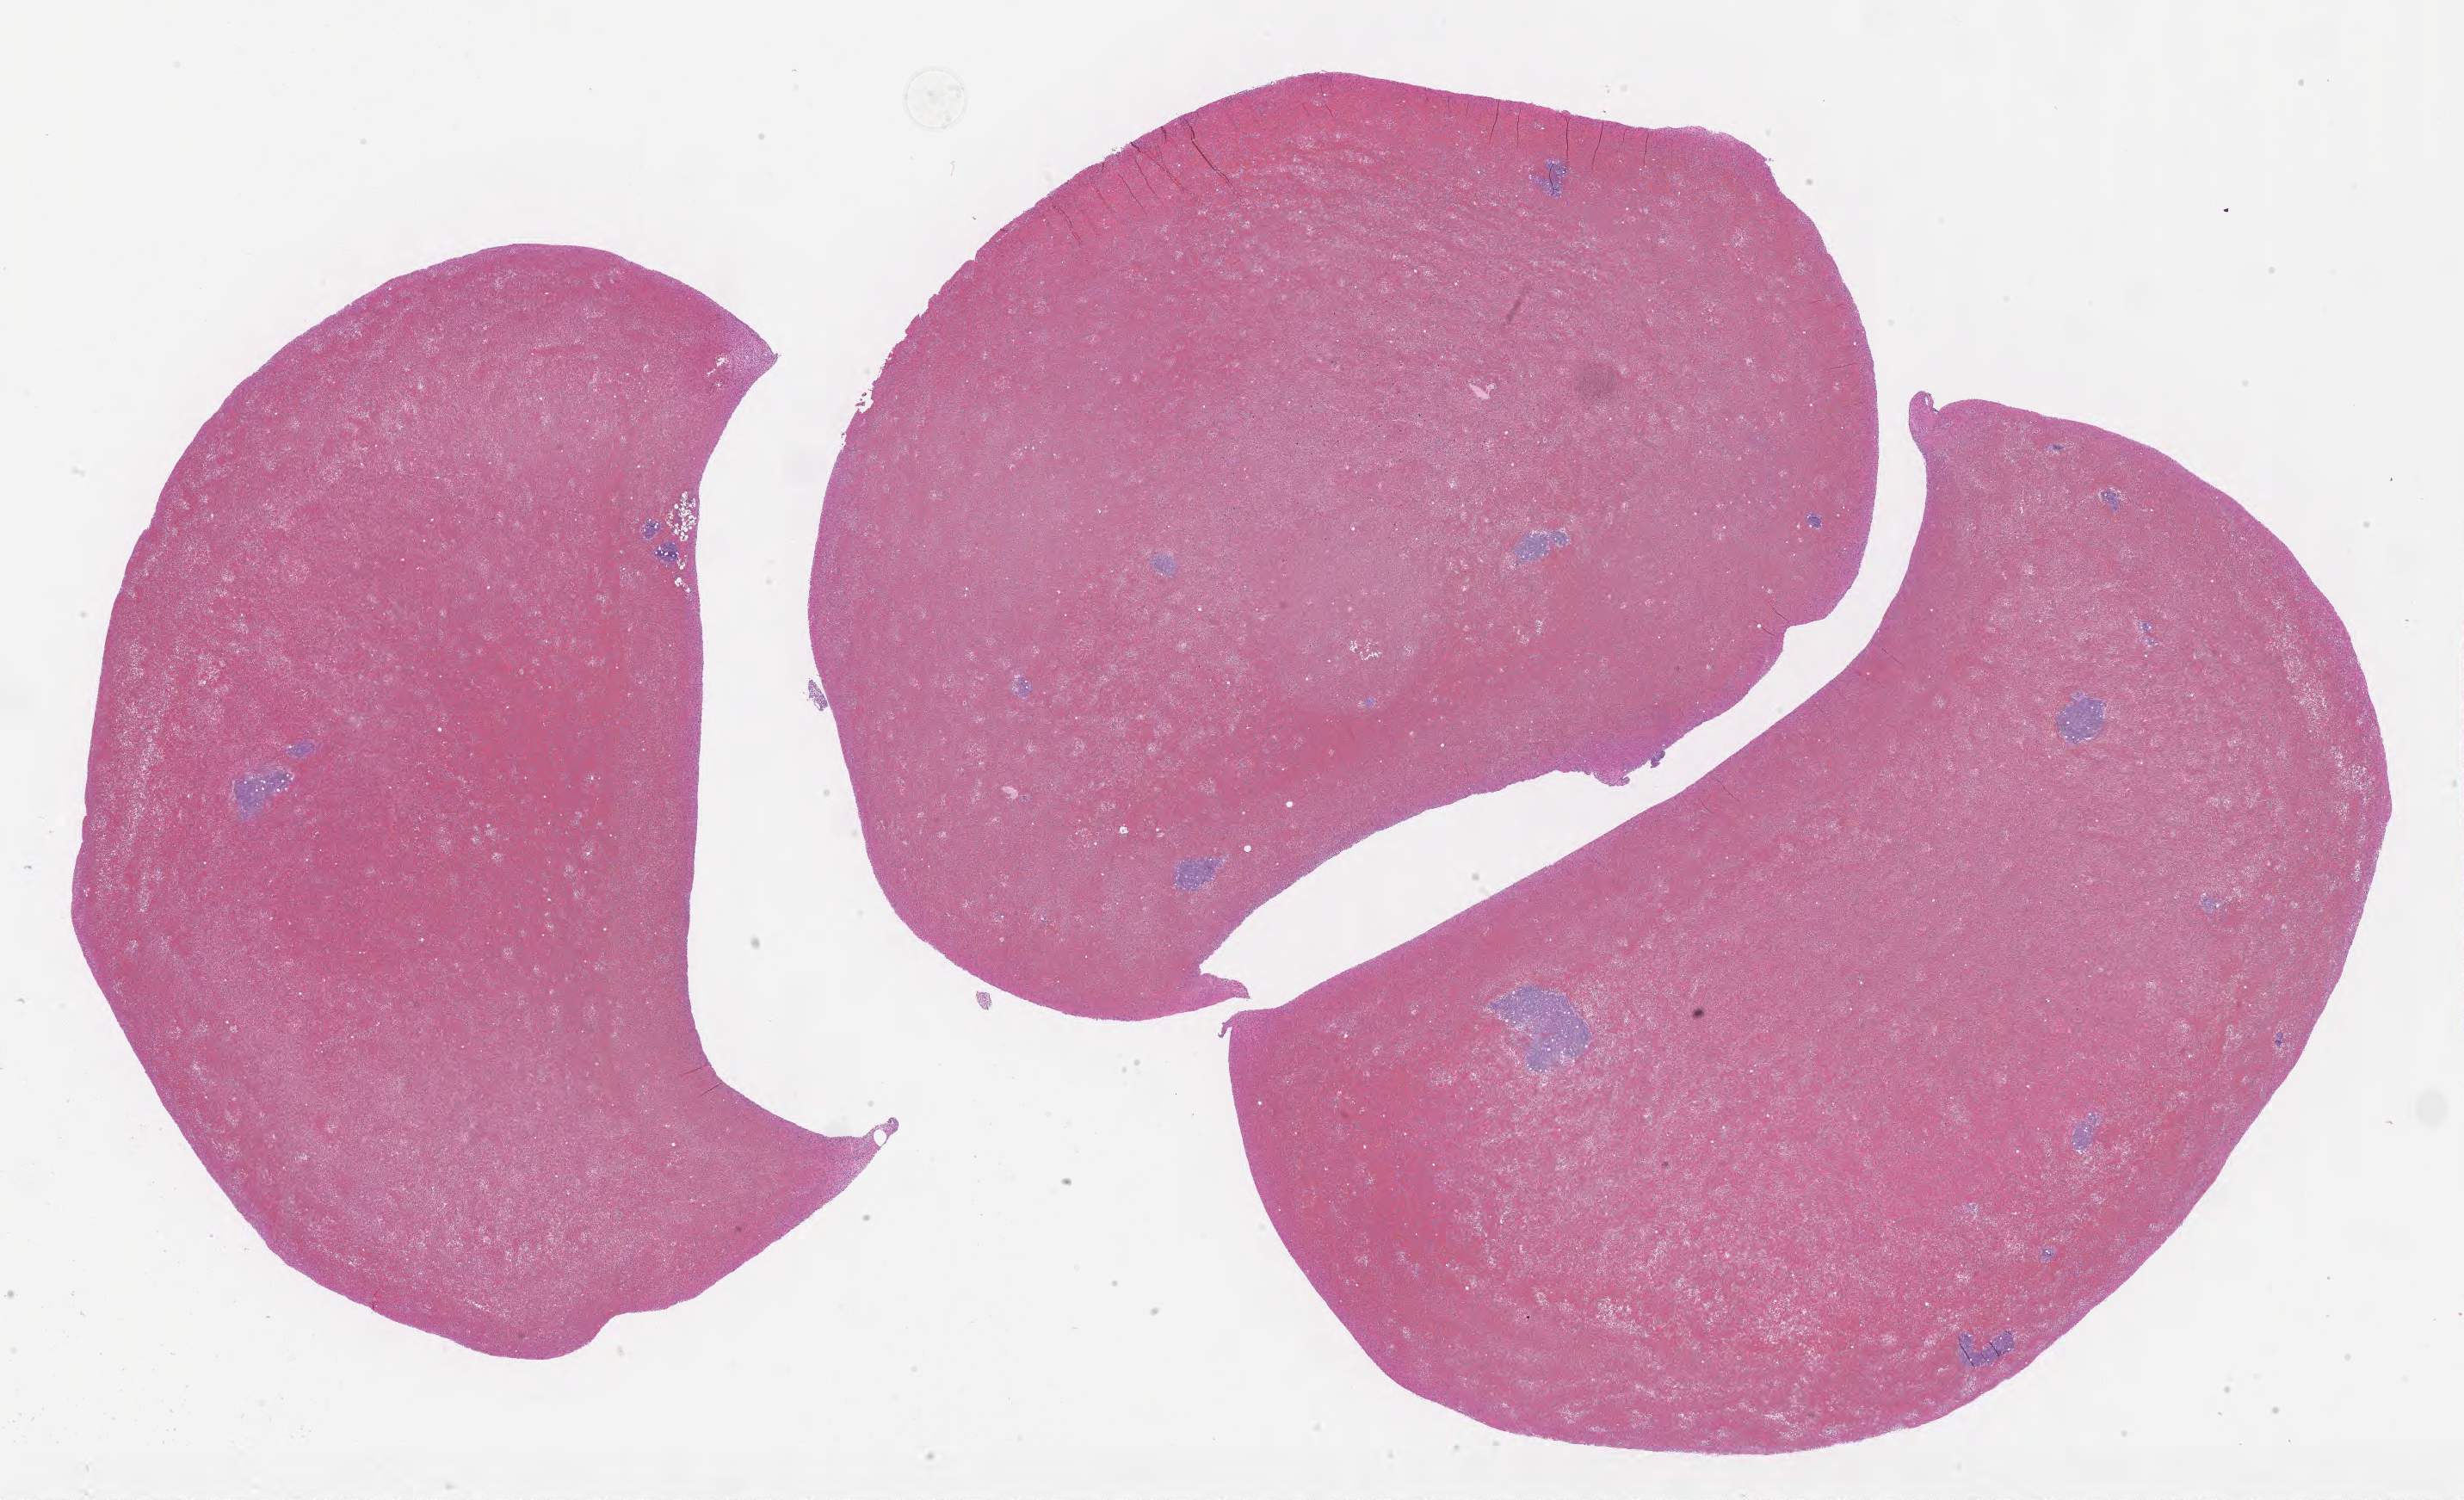
Whole-slide image, haematoxylin and eosin stain, low-resolution overview of the scanned area, about 23.1 x 14.1 mm, specimen: tumor tissue. Male patient, age 17 years.
Diagnosis: Burkitt lymphoma, NOS.